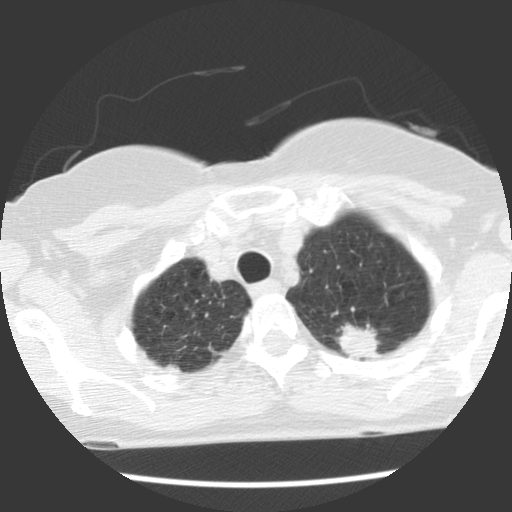
Low-dose screening chest CT, axial slice, baseline screening round, lung window (W 1500 / L -600 HU), 2.5 mm slice thickness, standard (soft-tissue) reconstruction kernel (STANDARD), slice 100 of 120 in the series. Female participant, aged 66 years at enrolment. Former smoker at enrolment.
• Expert-annotated lung lesion, box from (x=318, y=306) to (x=387, y=367) px.
• The exam's reader record, not a measurement of the box and not confirmed to be the same lesion: non-calcified nodule or mass ≥4 mm, left upper lobe, 22 × 17 mm, spiculated (stellate) margins, soft tissue attenuation.
• Lung cancer was diagnosed 50 days after this screen: adenocarcinoma, NOS, left upper lobe, poorly differentiated (G3), stage IB (AJCC 6th edition), 40 mm at pathology.